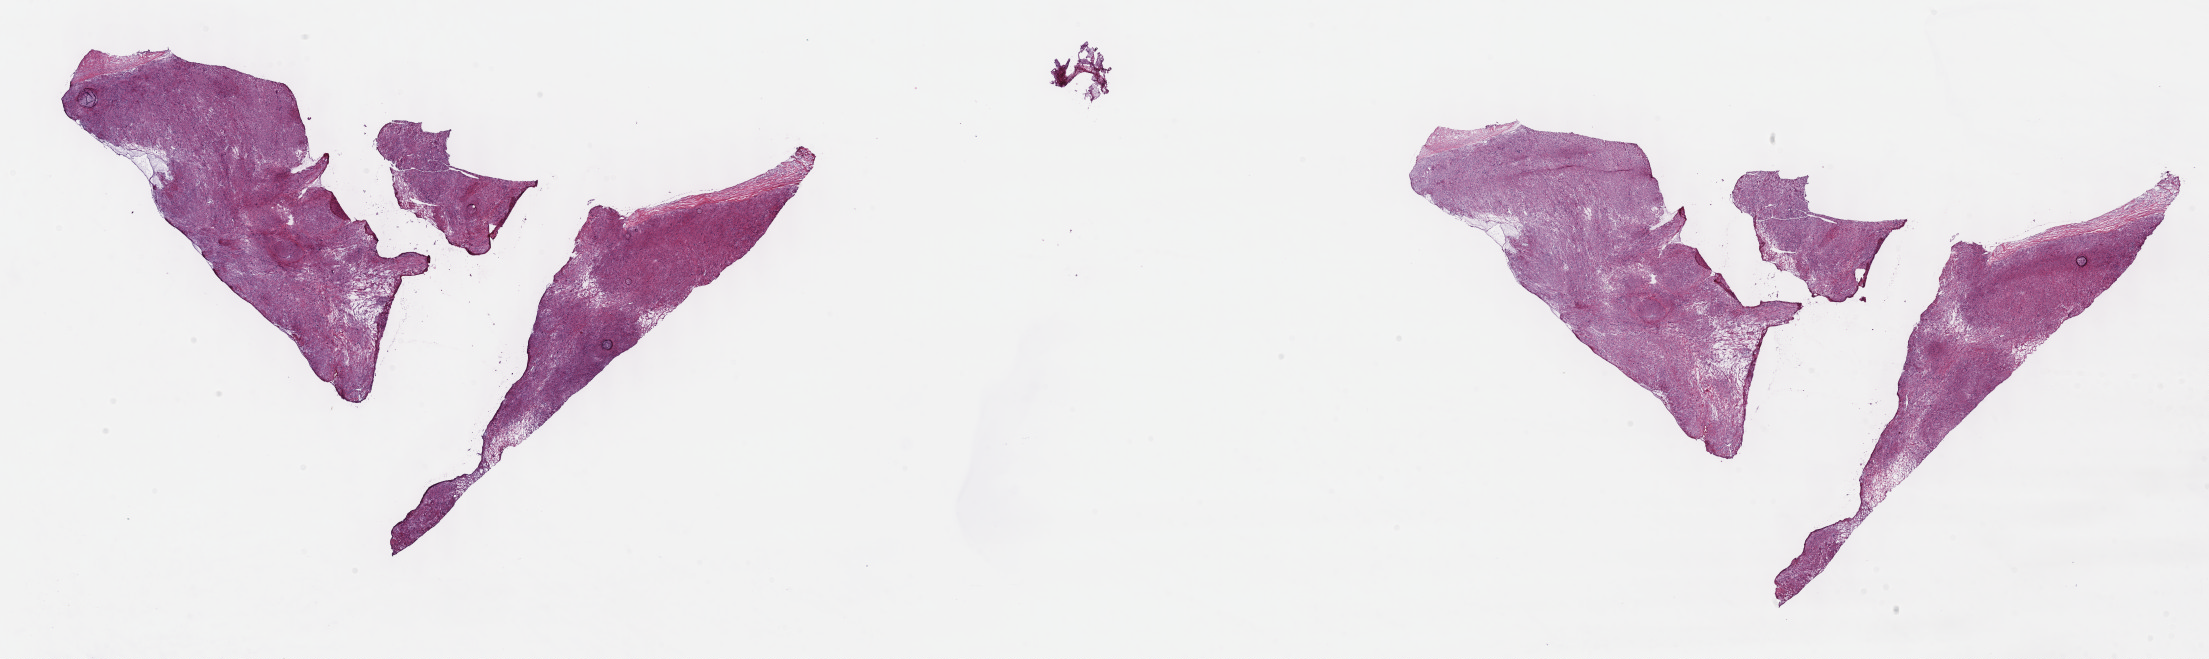
Digitized Hematoxylin and eosin (H&E) stained tissue section (whole slide), a low-resolution overview of the entire scanned area, about 35.7 x 10.7 mm (slide scanned at 40x); frozen section; sample: primary tumour, retroperitoneum and peritoneum. Female patient; age at initial diagnosis 63 years. Composition of this section per pathologist review: tumour cells 100%, tumour nuclei 80%.
Diagnosis: Leiomyosarcoma, NOS.